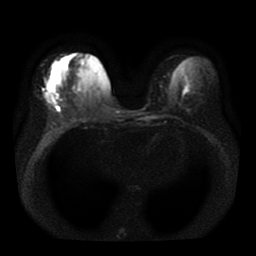
Breast MRI, one axial slice. Position 15 of 41 along the scan axis. Diffusion-weighted series; image 2 of 4 stored at this slice position (different b-values; order by instance number). 1.5 T. 256 × 256 image matrix, field of view 330 × 330 mm. Female patient.
Structures marked on this image (manually delineated by an expert):
- tumour on diffusion-weighted imaging: bounding box (x1, y1, x2, y2) in pixels: (44, 85, 58, 104)